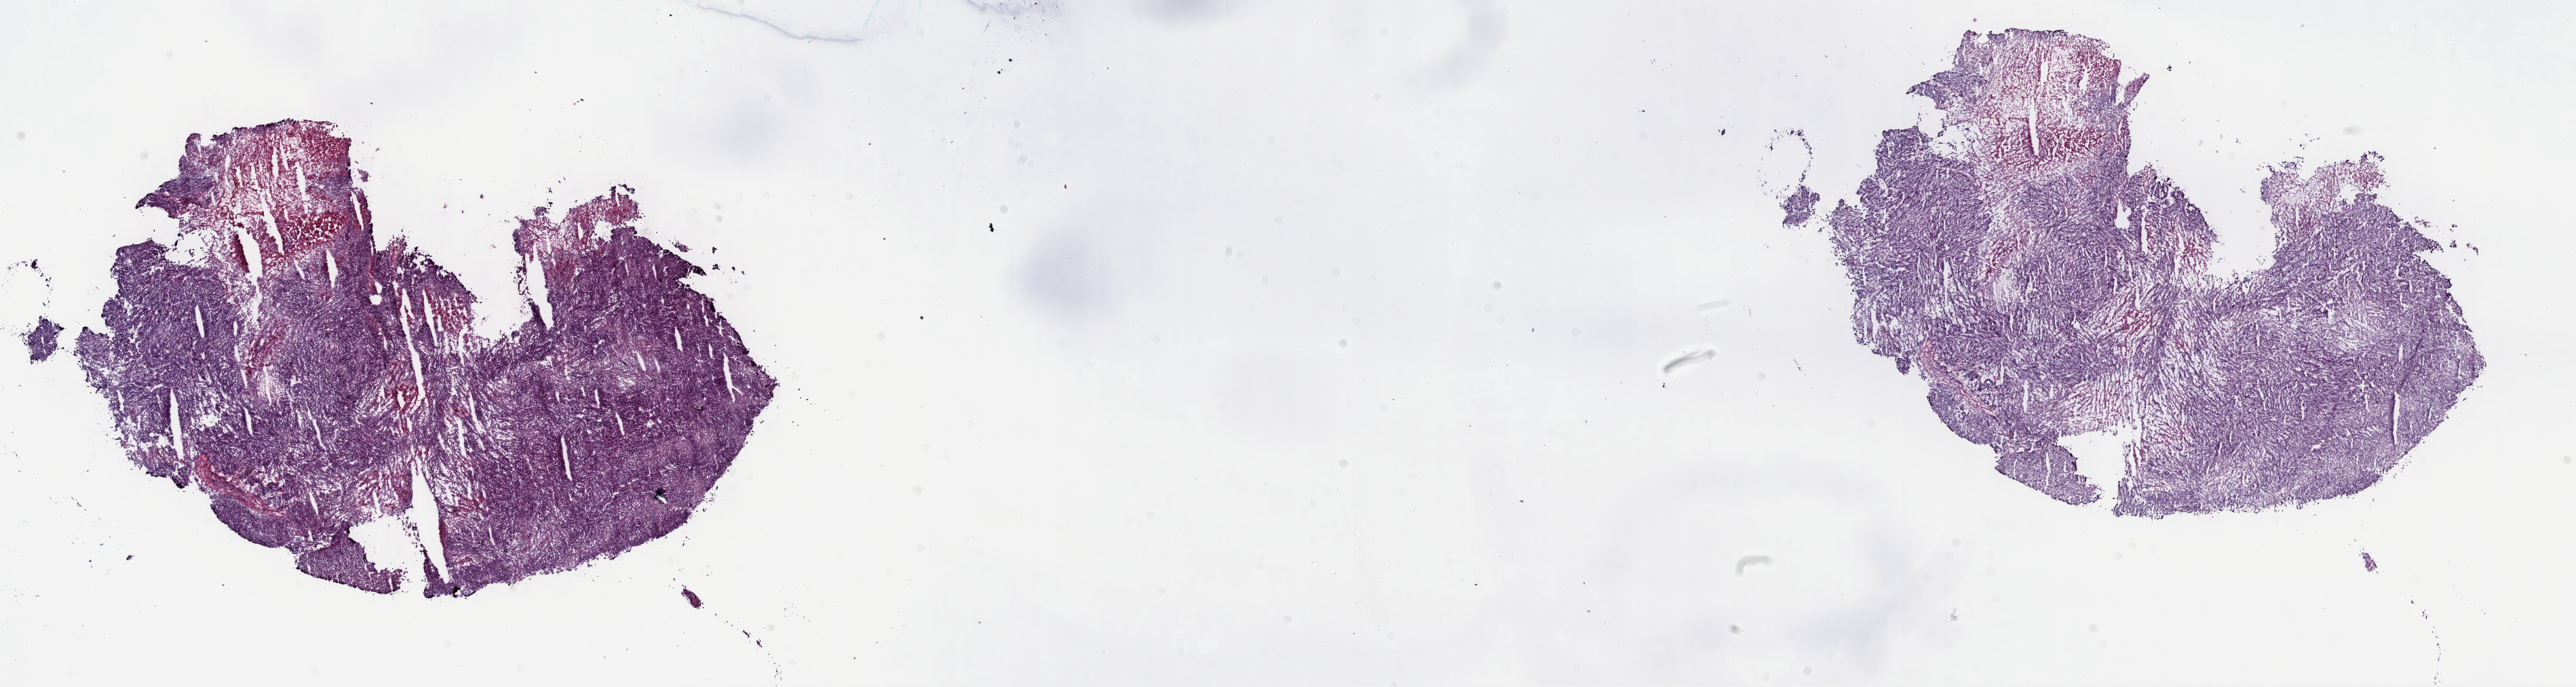
Whole-slide histology image, H&E — low-resolution overview of the scanned area, about 30.7 x 8.2 mm; frozen section from the top of the tissue portion; liver, primary tumour sample. Patient: female, age at initial diagnosis 66 years.
Diagnosis: Hepatocellular carcinoma, NOS.